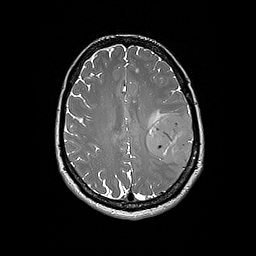
Brain MRI from a brain-tumour surgery series, one axial slice. Position 74 of 192 along the scan axis. 1 mm slice thickness. 256 × 256 image matrix. From the clinical record (not read from this slice): histopathology: Glioblastoma; WHO grade: 4; IDH mutation: no.
Structures marked on this image (manually delineated by an expert):
- tumour: bounding box (x1, y1, x2, y2) in pixels: (146, 113, 194, 165)